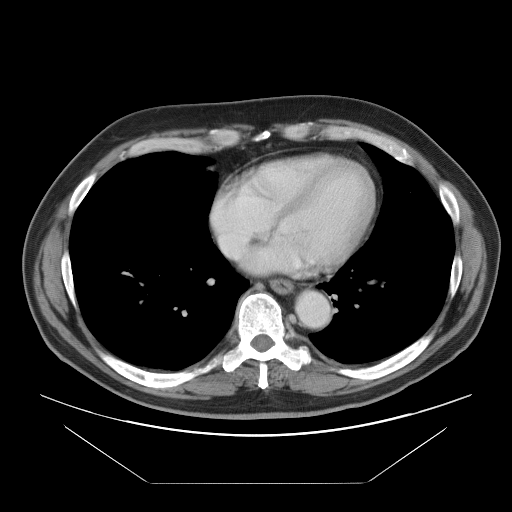
Contrast-enhanced abdominal CT, one axial slice; position 95 of 97 along the scan axis; intravenous contrast given; soft-tissue window (W 400 / L 40 HU); 5 mm slice thickness; 512 × 512 image matrix, field of view 442 × 442 mm. Male patient, age 62 years. From the clinical record (not read from this slice): diagnosis: colorectal cancer liver metastases, imaged before liver resection.
Outlined on this slice (expert manual segmentation):
- hepatic veins: bounding box (x1, y1, x2, y2) in pixels: (213, 183, 247, 267)